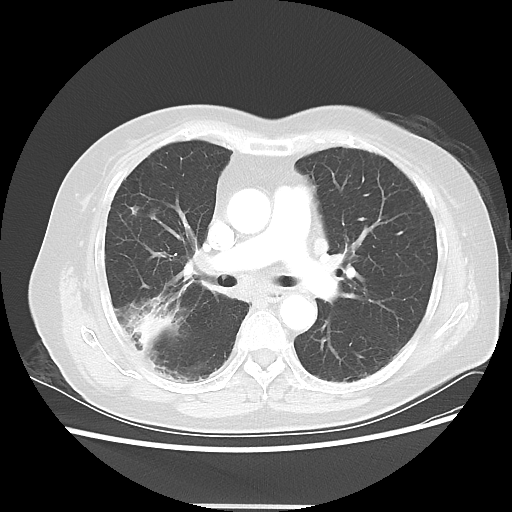
Chest CT, one axial slice; position 28 of 50 along the scan axis; reconstruction kernel LUNG; lung window (W 1500 / L -600 HU); 5 mm slice thickness; 512 × 512 image matrix, field of view 360 × 360 mm. Female patient, age 72 years. Case-level facts recorded for this patient, not image findings: clinical TNM (as recorded): T2 N1 M0; histopathological grade: G1.
Structures marked on this image (bounding box drawn by a radiologist):
- lung tumour (recorded histology: adenocarcinoma): bounding box (x1, y1, x2, y2) in pixels: (128, 311, 174, 350)